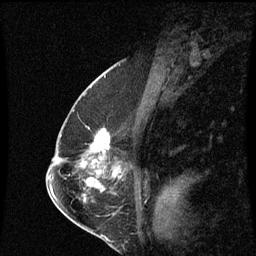
Breast MRI (dynamic contrast-enhanced), one sagittal slice; position 36 of 60 along the scan axis; dynamic contrast-enhanced series, image 2 of 3 at this slice position (ordered by acquisition); 1.5 T; TE 4.2 ms, TR 8.9 ms; 2 mm slice thickness; 256 × 256 image matrix, field of view 200 × 200 mm. Patient: female, 57 years. From the clinical record (not read from this slice): setting: breast cancer imaged before/during neoadjuvant chemotherapy; receptor status: HR-positive, HER2-negative.
Annotated regions visible in this slice (semi-automatic segmentation, software-assisted and operator-edited):
- analysis volume of interest (the breast-tissue region the enhancement analysis was run in; not a lesion): bounding box <83,130,108,159> (left, top, right, bottom; pixels)
- tumour enhancement mask (voxels above the 70 % enhancement threshold inside the analysis volume of interest): <94,132,108,159>